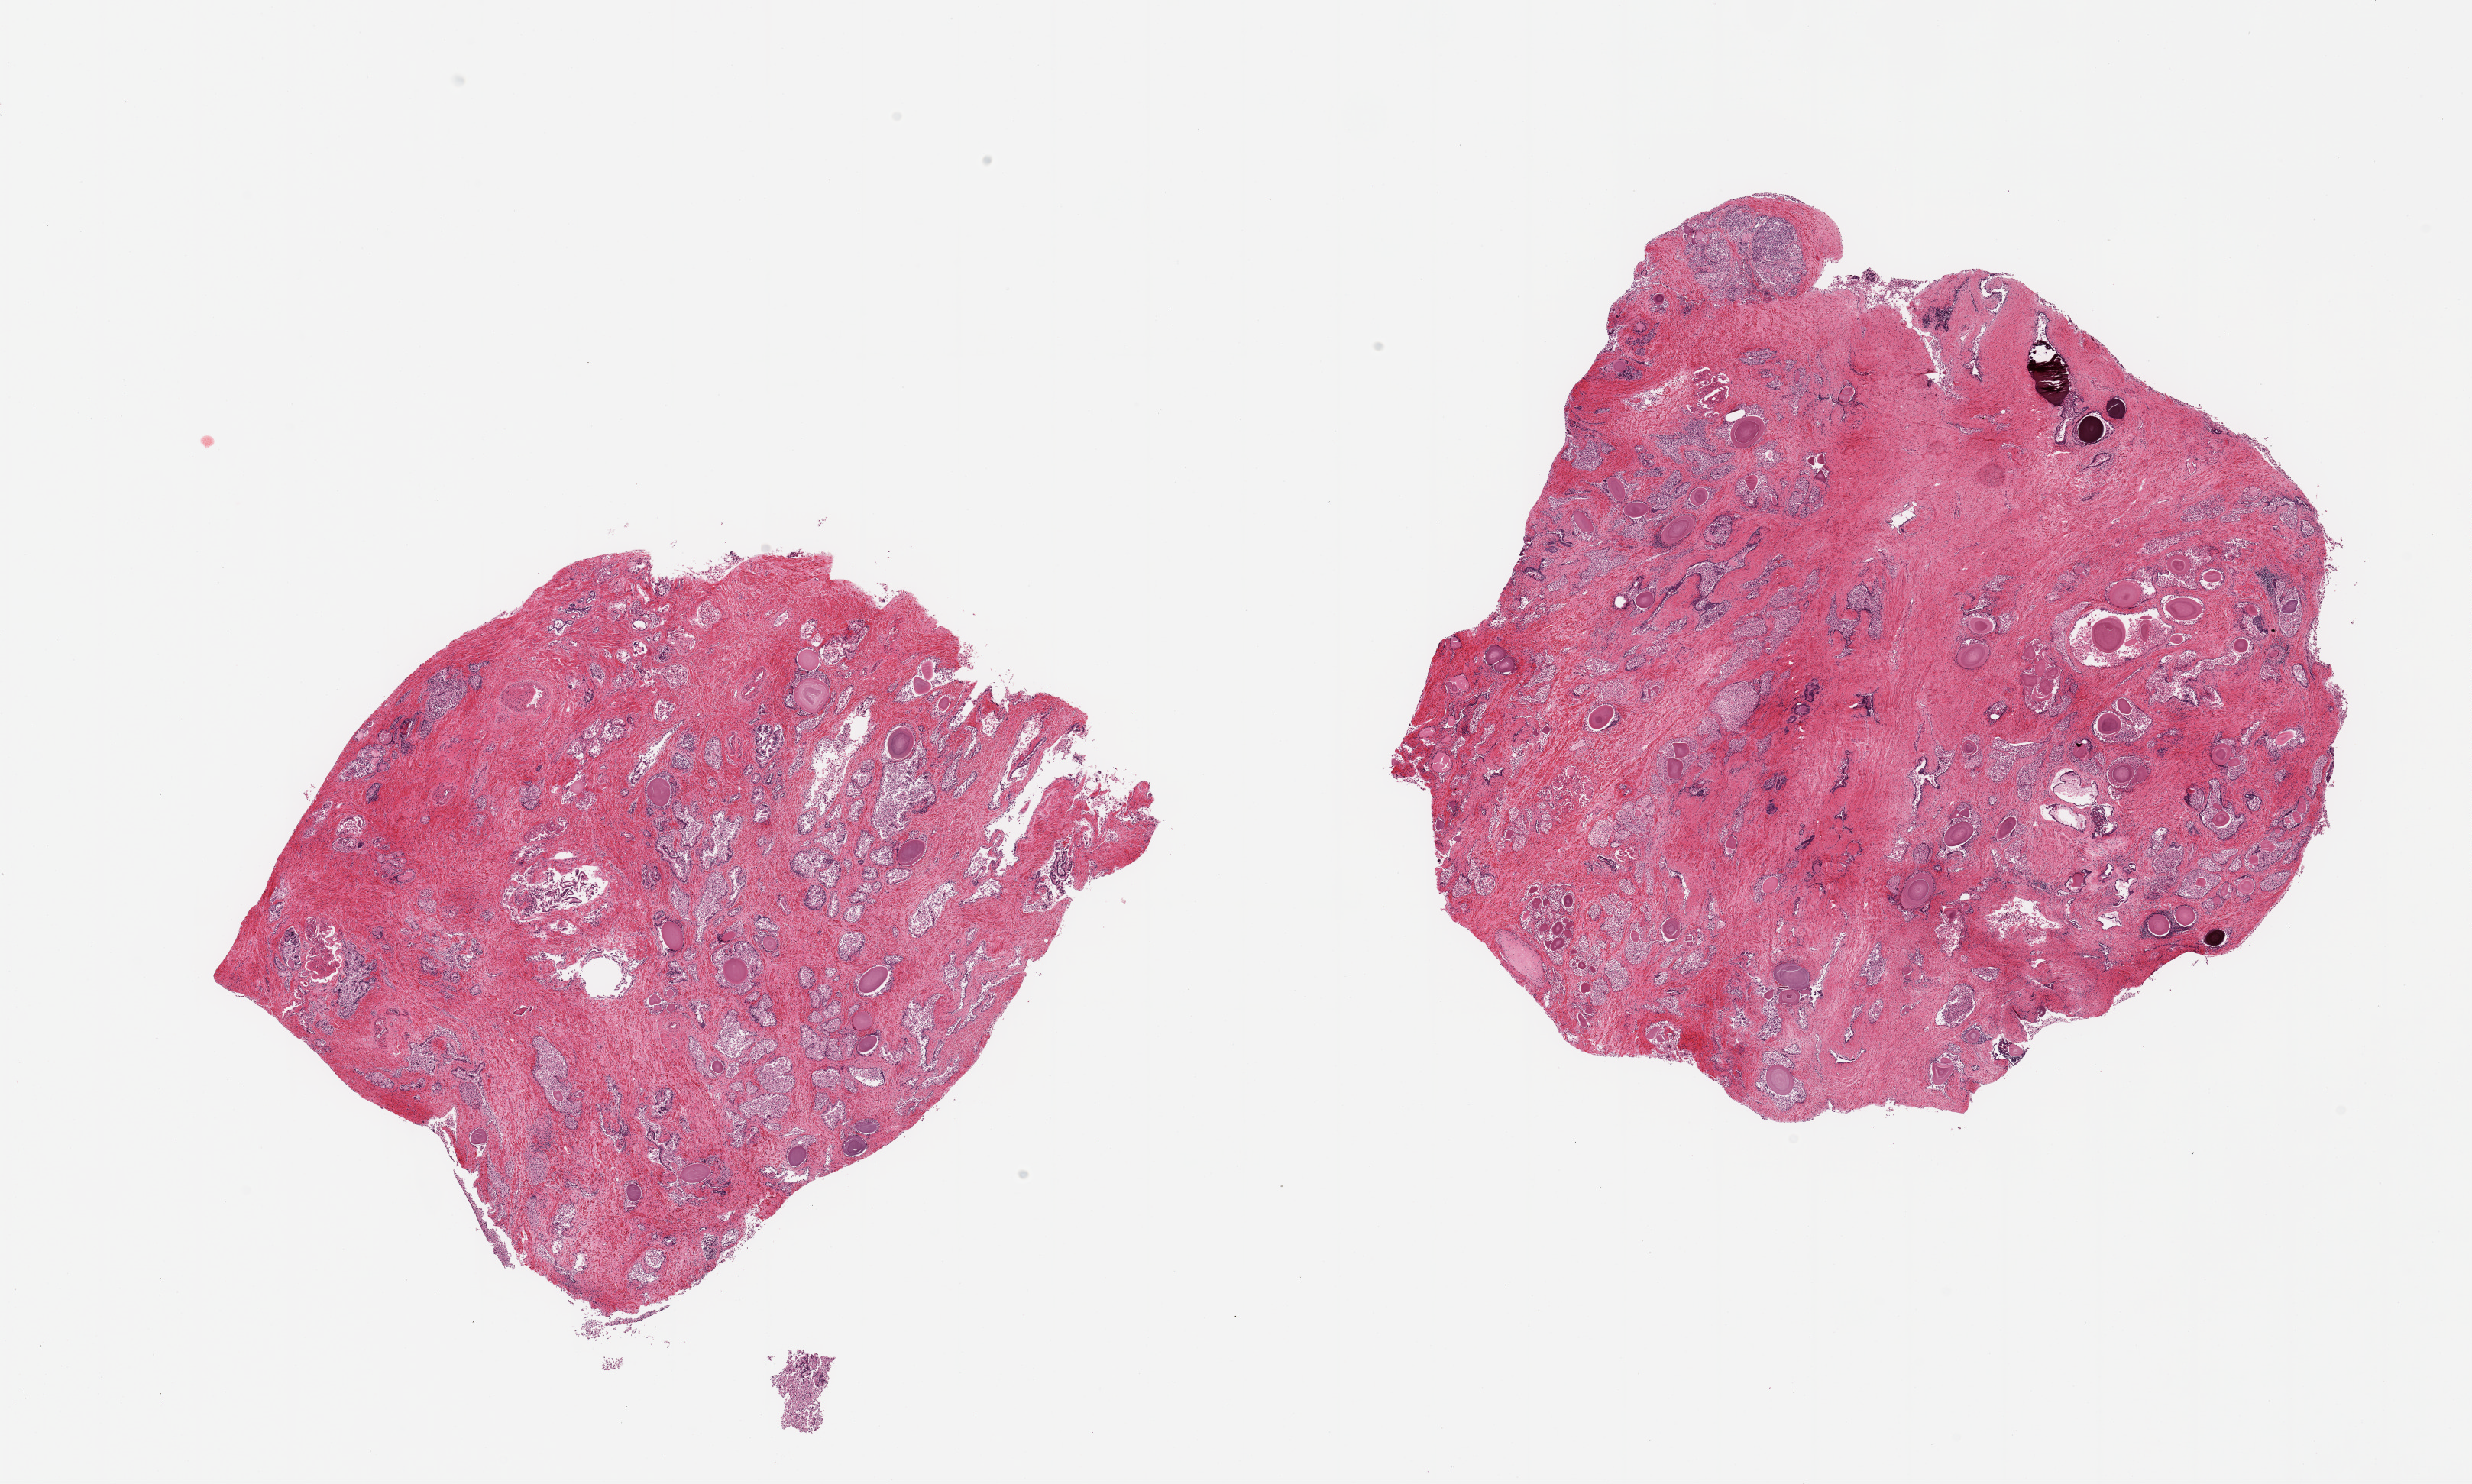
Whole-slide image, hematoxylin and eosin (H&E) stain, brightfield — low-resolution overview of the scanned area, about 25.6 x 15.4 mm (acquisition: 20x scan), PAXgene-fixed paraffin-embedded (PFPE) section, section of prostate (target tissue), donor tissue sample. Donor sex: male.
Reviewer comment on this tissue sample: 2 pieces, glandular elements with advanced autolysis, hyperplastic pattern.